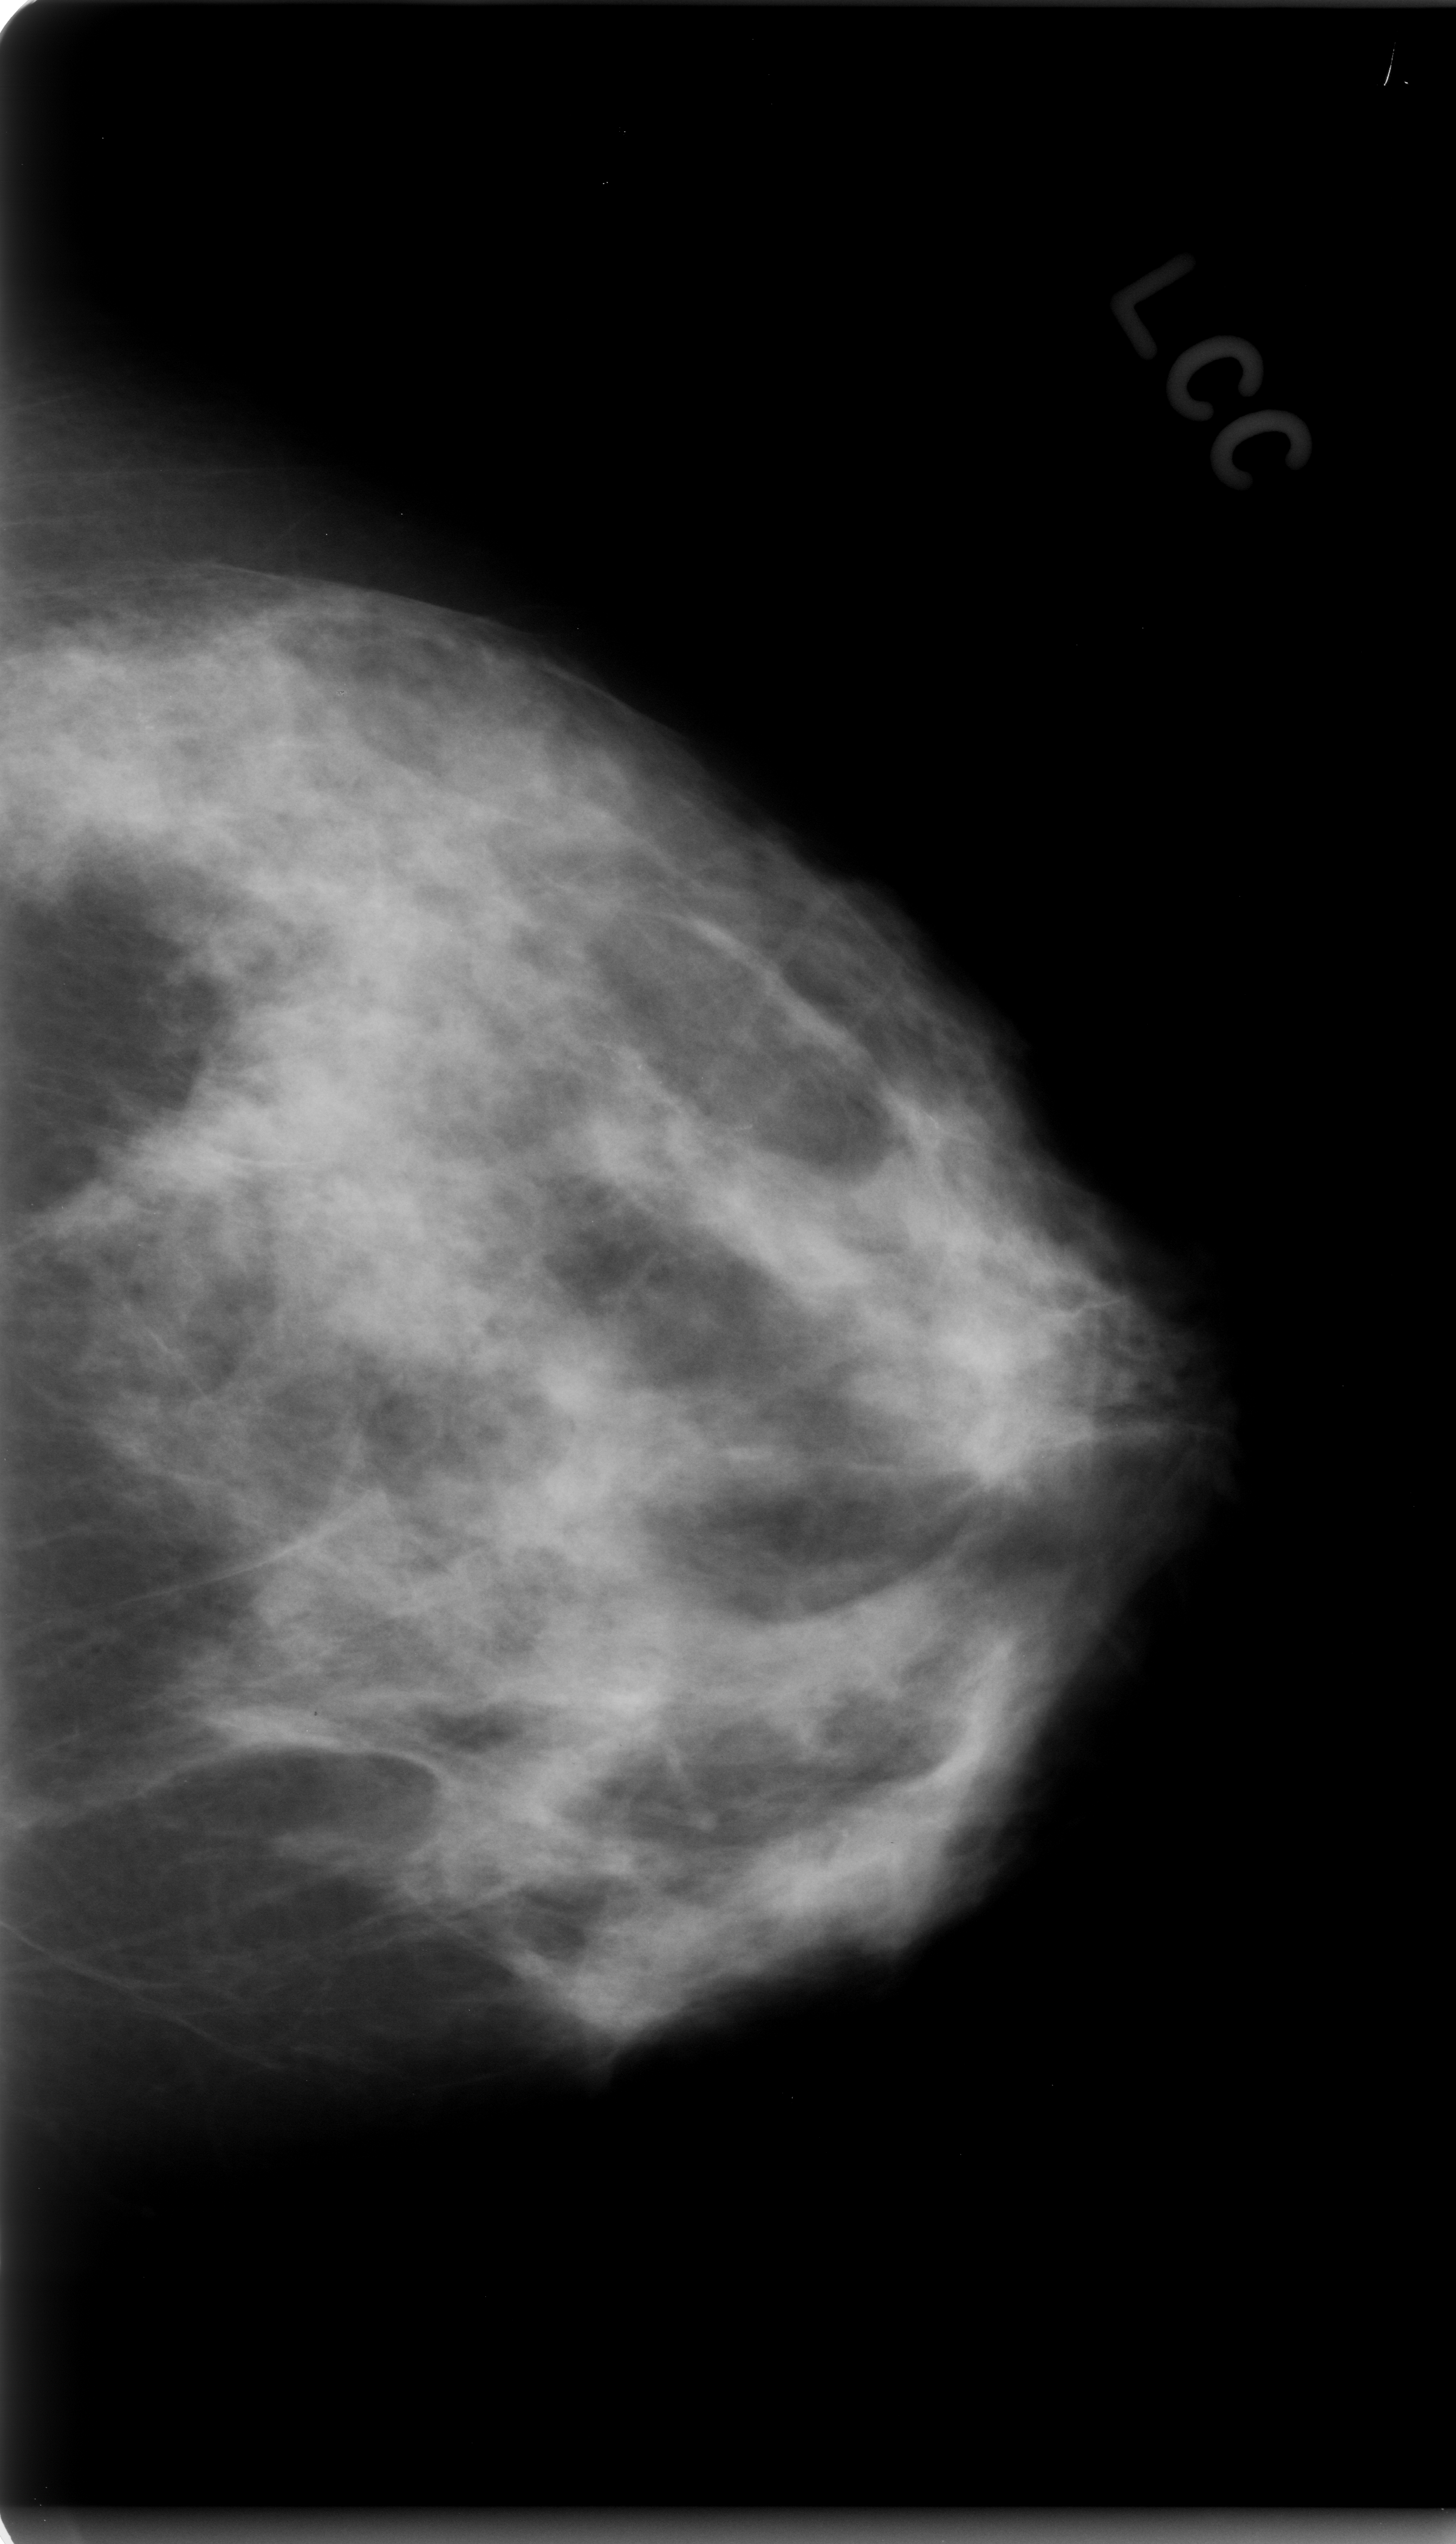
Digitized screen-film mammogram, left breast, CC view, BI-RADS breast density category 3 (scale 1–4).
- Radiologist-marked abnormalities on this image: Finding 1 of 2: calcifications, morphology amorphous, distribution clustered; BI-RADS assessment category 4; pathology (as recorded): benign.
- Finding 2 of 2: calcifications, morphology amorphous, distribution clustered; BI-RADS assessment category 4; pathology (as recorded): malignant.